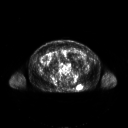
FDG PET of an extremity soft-tissue mass (from a PET/CT study), one axial slice; slice 96 of 267 in the series (ordered by position); 3.27 mm slice thickness; 128 × 128 image matrix. Patient: male, 61 years. Case-level facts recorded for this patient, not image findings: histological type: pleiomorphic leiomyosarcoma; grade: high; site of the primary tumour: left buttock.
Outlined on this slice (expert contour drawn on MRI and transferred to this co-registered scan by the dataset authors):
- gross tumour volume including surrounding oedema: bounding box [x1, y1, x2, y2] px = [76, 85, 81, 91]
- gross tumour volume (mass): [77, 86, 81, 90]